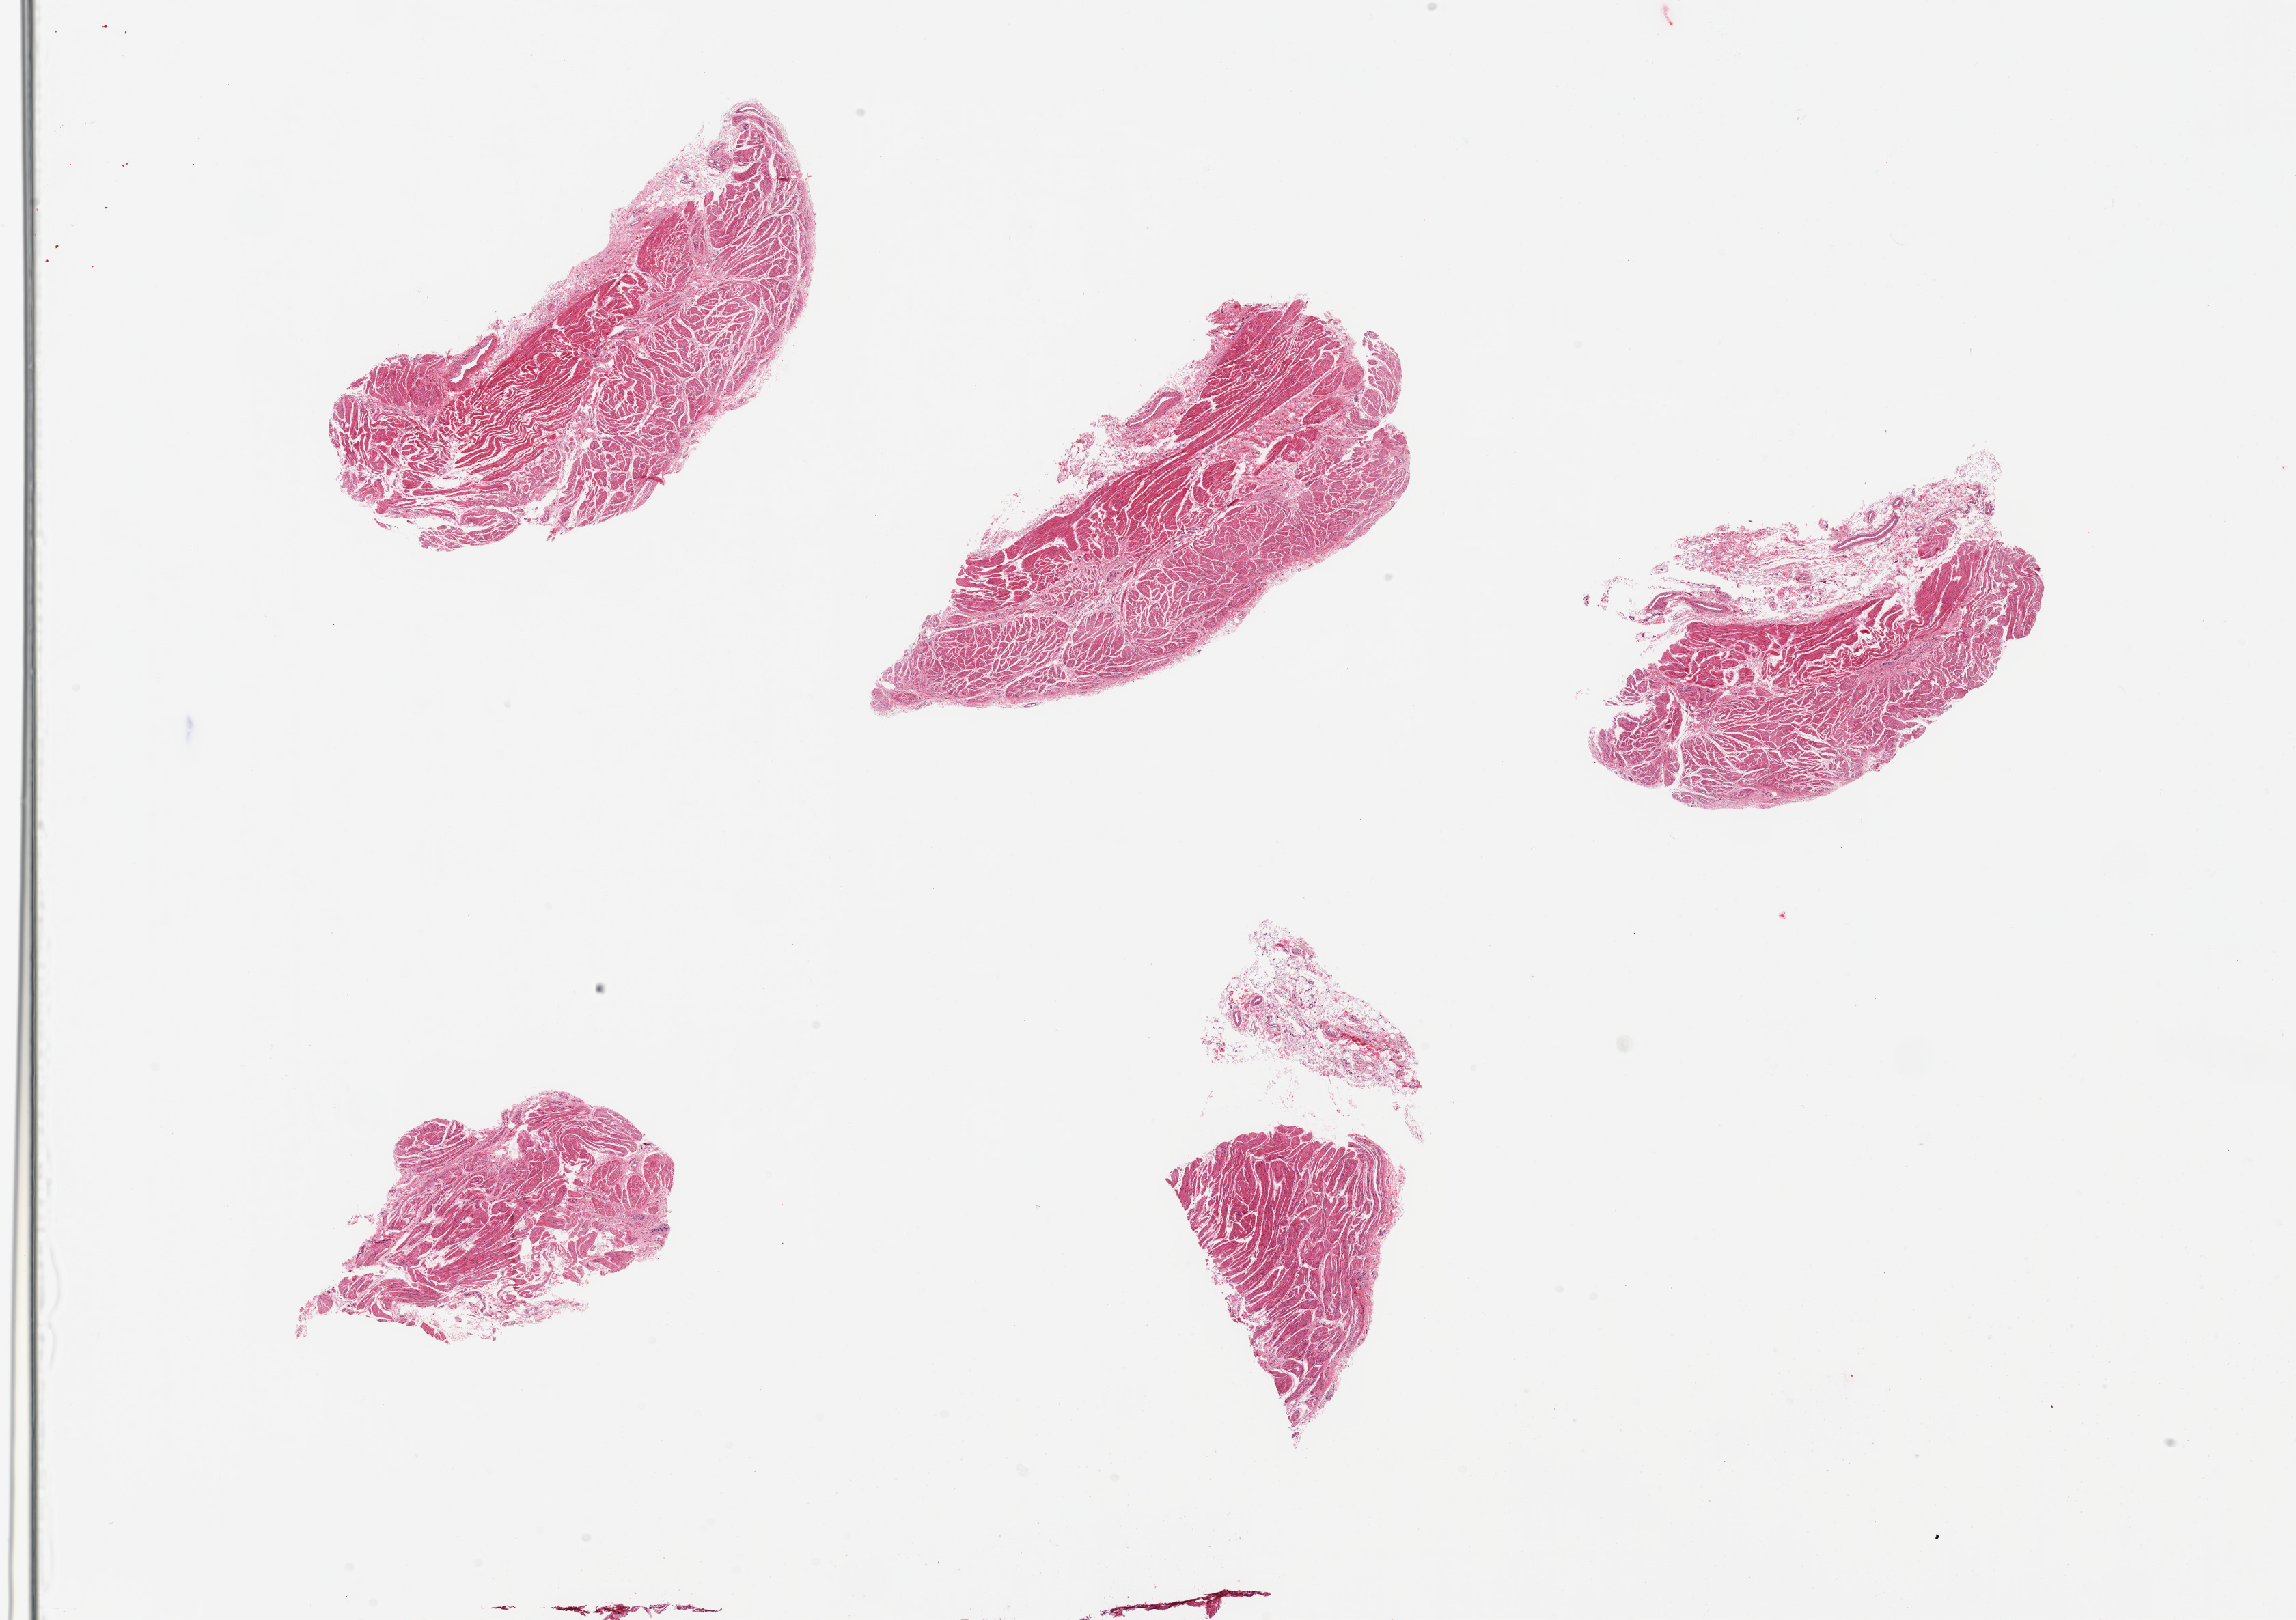
Digitized hematoxylin and eosin (H&E)-stained section, brightfield — shown as a low-resolution overview of the whole scanned area (about 26.6 x 18.8 mm); PAXgene-fixed, paraffin-embedded tissue; sampled site (target tissue): gastroesophageal junction; tissue donor sample. Donor sex: male.
Reviewer comment on this tissue sample: 5 pieces; target muscularis.